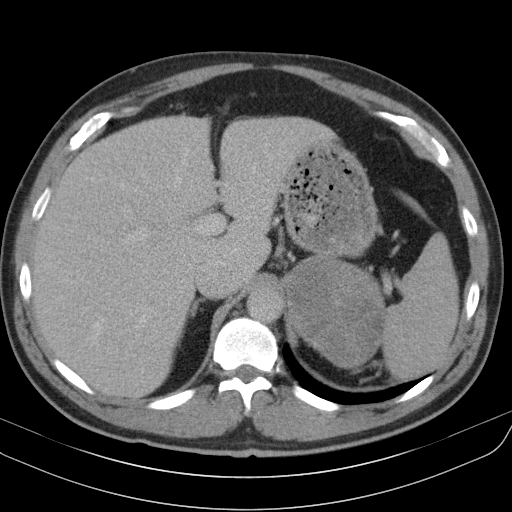
Contrast-enhanced abdominal CT, one axial slice; position 76 of 91 along the scan axis; reconstruction kernel B31s; soft-tissue window (W 400 / L 40 HU); 5 mm slice thickness; 512 × 512 image matrix, field of view 370 × 370 mm. Patient: male, 51 years. From the clinical record (not read from this slice): diagnosis: adrenocortical carcinoma; tumour side: left adrenal; tumour size at pathology: 18 cm; Ki-67 index: 40 %; stage (as recorded): 3.
Annotated regions visible in this slice (semi-automatically segmented with operator editing):
- mass: bounding box (x1, y1, x2, y2) in pixels: (284, 259, 383, 367)